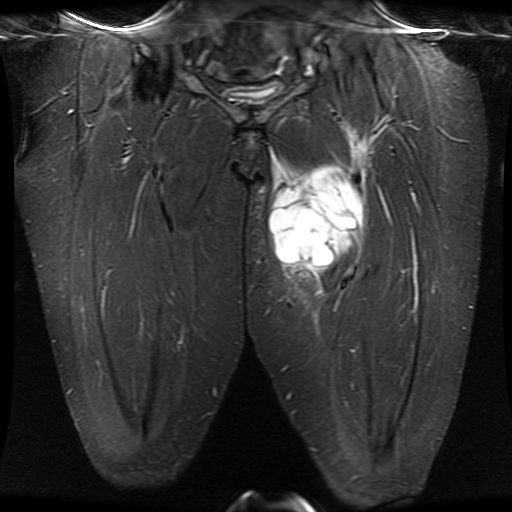
MRI of an extremity soft-tissue mass, one coronal slice; position 10 of 30 along the scan axis; STIR; 5 mm slice thickness; 512 × 512 image matrix, field of view 460 × 460 mm. Female patient. From the clinical record (not read from this slice): histological type: myxofibrosarcoma; grade: intermediate; site of the primary tumour: left thigh.
Annotated regions visible in this slice (outlined manually by an expert reader):
- gross tumour volume including surrounding oedema: bounding box [x1, y1, x2, y2] px = [269, 125, 371, 311]
- gross tumour volume (mass): [269, 167, 365, 289]